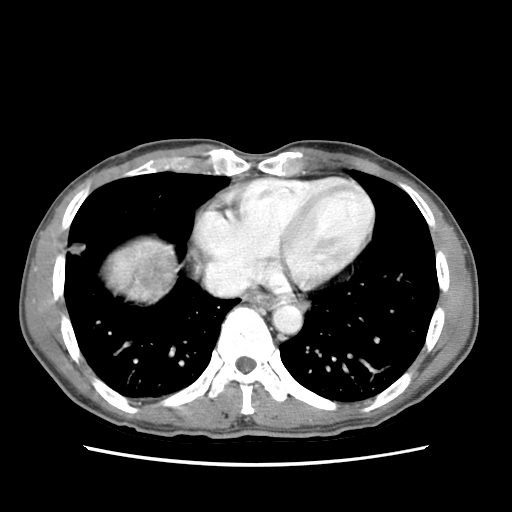
Contrast-enhanced abdominal CT (liver protocol), one axial slice; slice 72 of 79 in the series (ordered by position); reconstruction kernel STANDARD; 120 kVp; soft-tissue window (W 400 / L 40 HU); 2.5 mm slice thickness; 512 × 512 image matrix, field of view 320 × 320 mm. Case-level facts recorded for this patient, not image findings: diagnosis: hepatocellular carcinoma (patient treated with transarterial chemoembolisation; whether this scan precedes or follows treatment is not stated here); TNM stage (as recorded): Stage-IIIB; Child-Pugh class: A; tumour differentiation: moderately differentiated.
Structures marked on this image (semi-automatic segmentation, software-assisted and operator-edited):
- liver parenchyma outside the tumour (the mass and vessels are separate outlines, so this box may not span the whole liver): bounding box [x1, y1, x2, y2] px = [131, 230, 167, 304]
- mass: [101, 231, 178, 306]